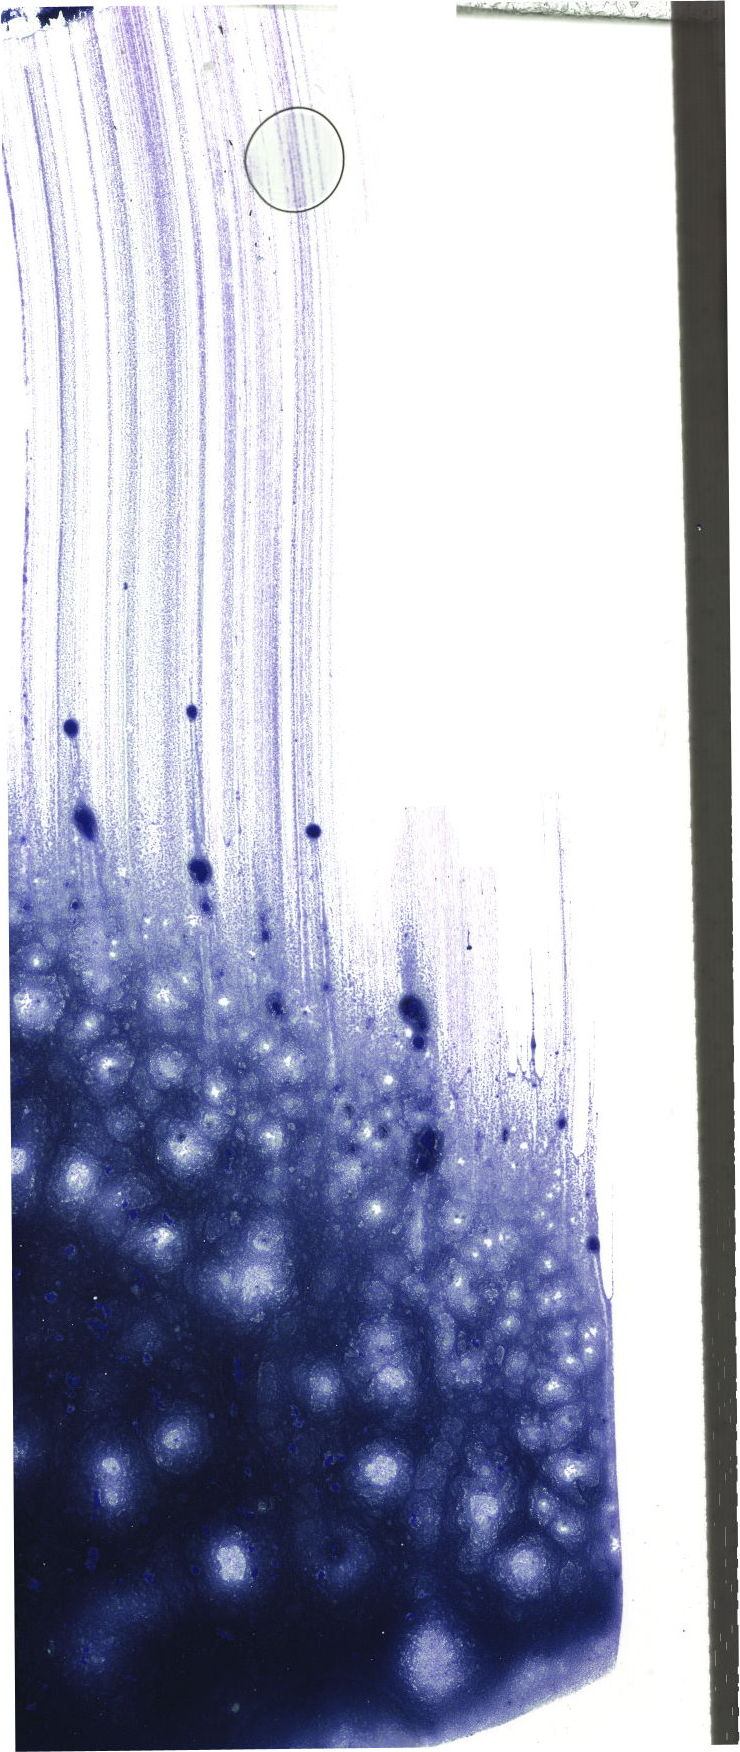
Whole-slide image of a May-Grünwald–Giemsa-stained bone marrow aspirate smear, low-resolution overview of the scanned area, about 21.0 x 49.7 mm. Patient sex: male.
- diagnosis: Chronic Phase Chronic Myeloid Leukemia, BCR-ABL1 Positive